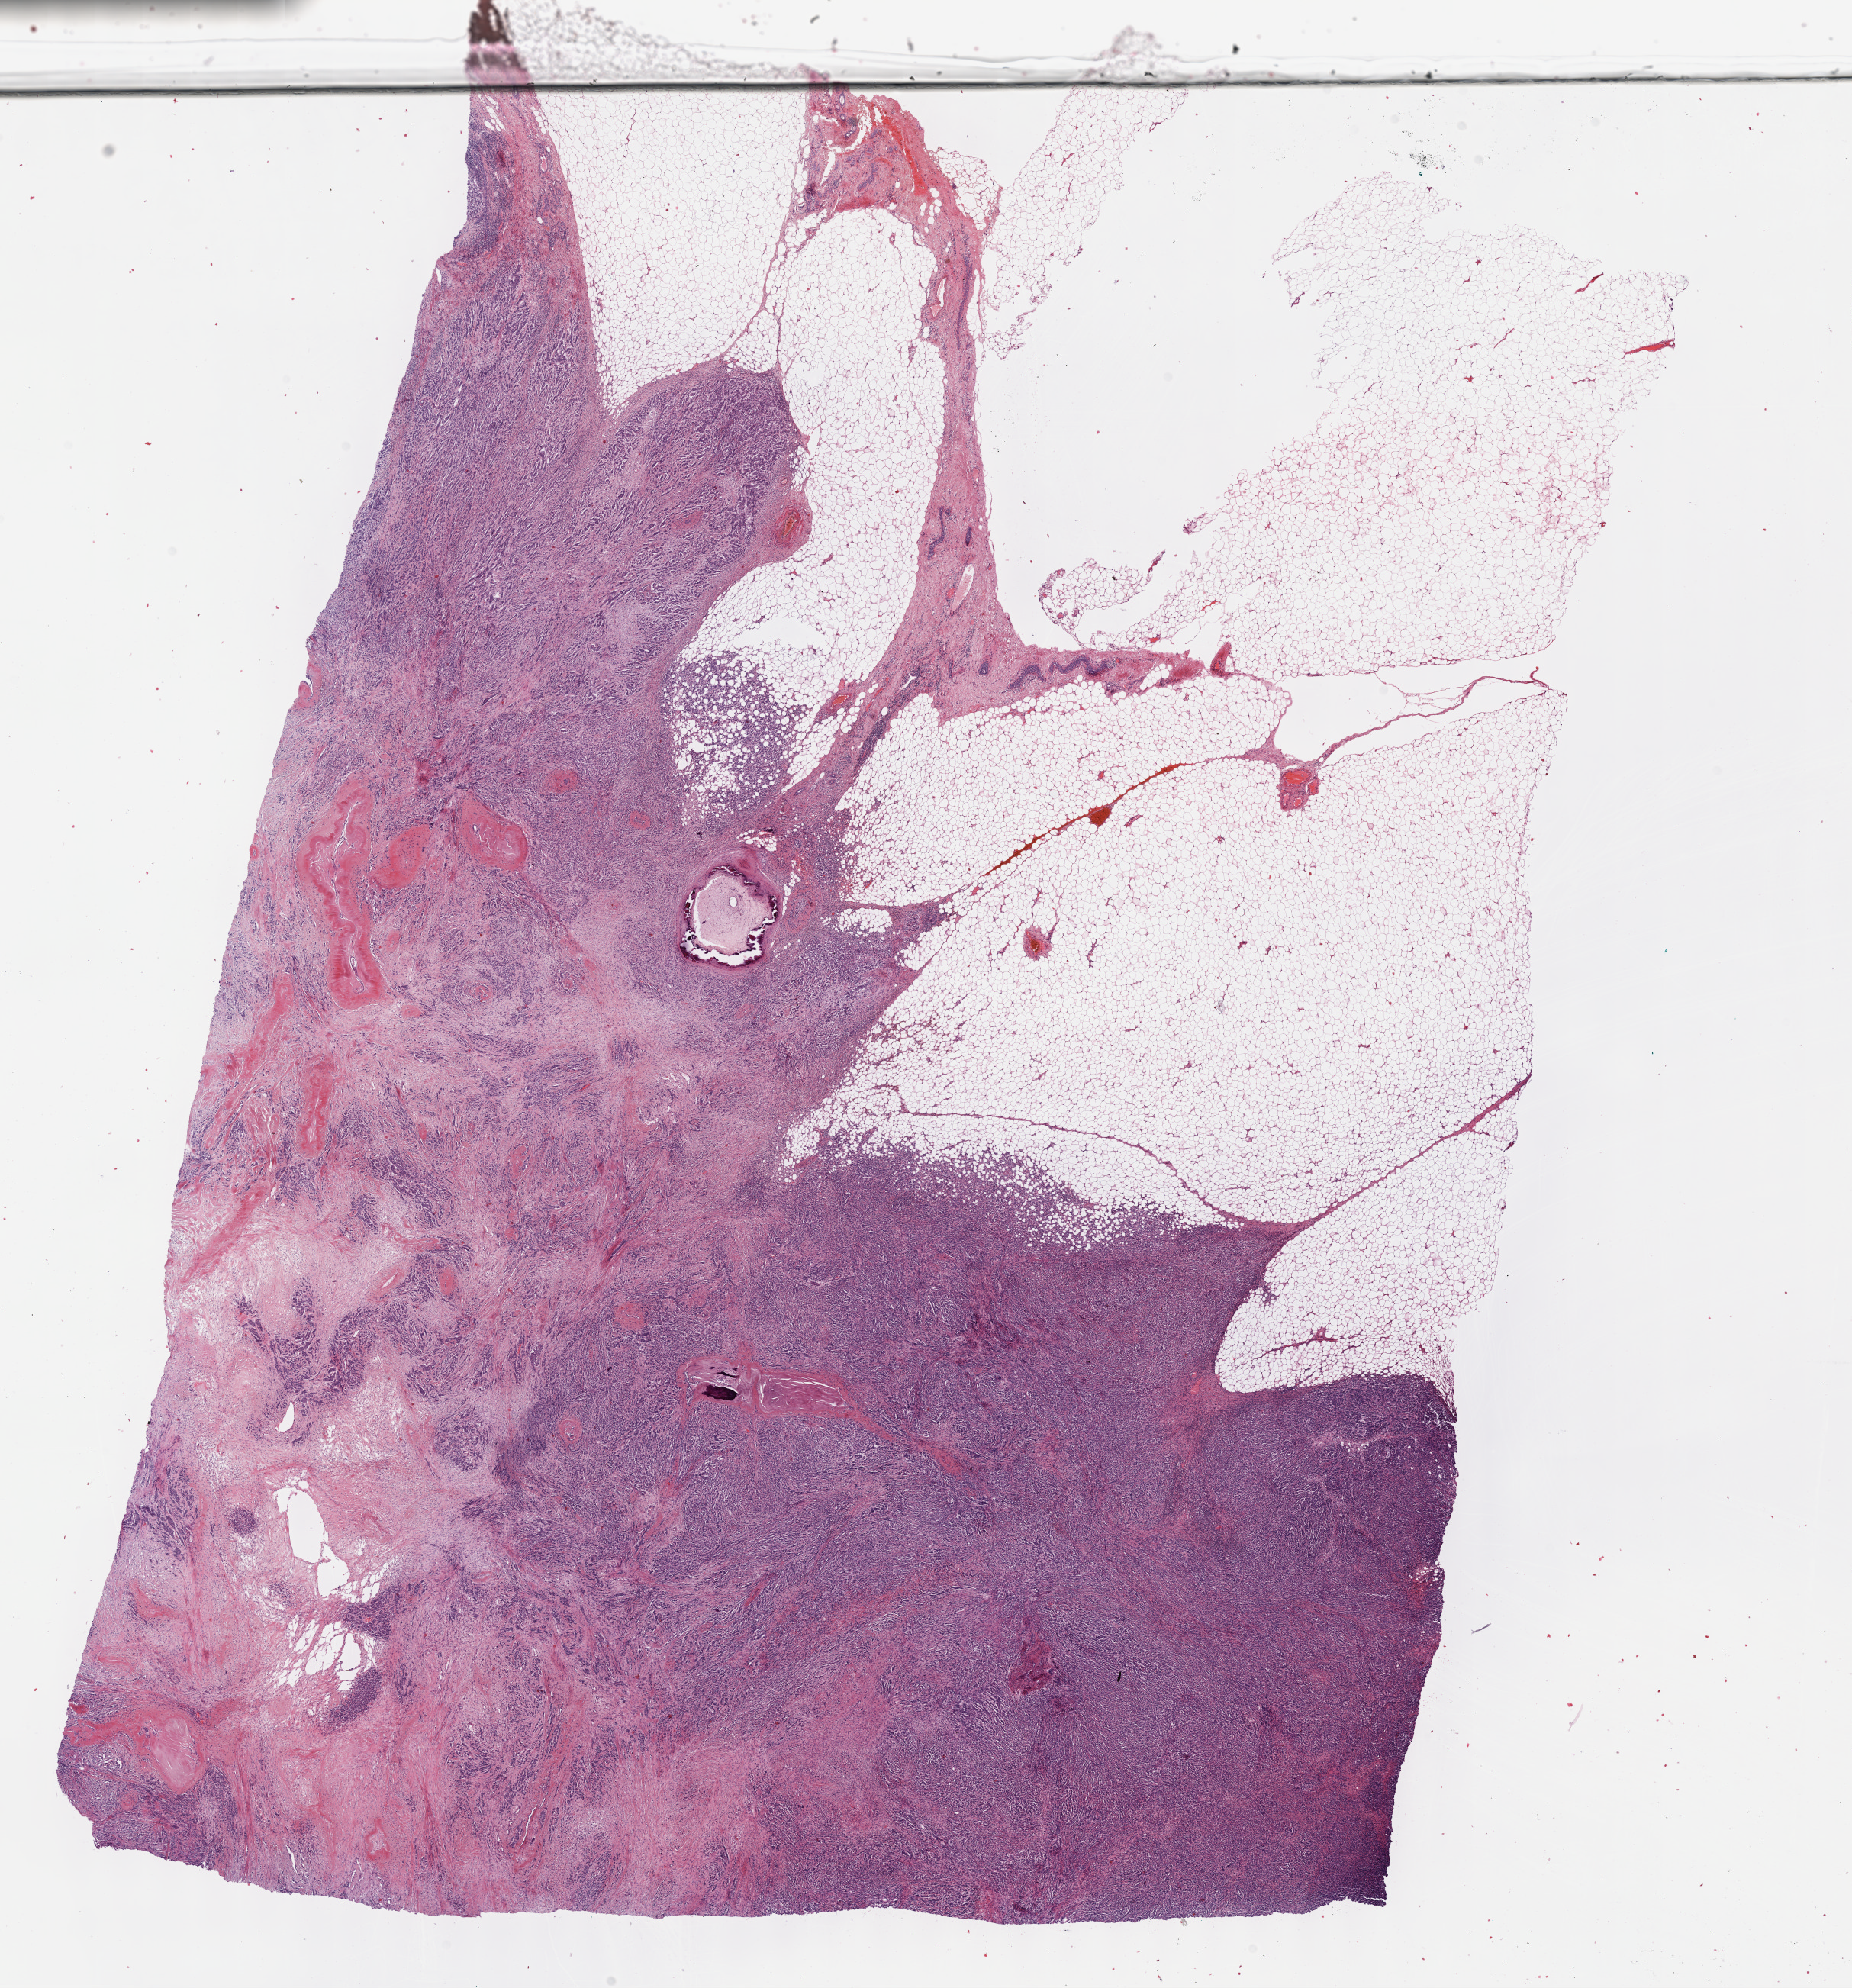
Digitized H&E tissue section (whole slide) — a low-resolution overview of the entire scanned area, about 19.6 x 21.1 mm, formalin-fixed paraffin-embedded (FFPE) diagnostic section, sample: primary tumour, breast. Female, age 80 years at initial diagnosis.
• laterality: left
• AJCC pathologic stage: IIIA (7th edition)
• histologic diagnosis: Infiltrating duct carcinoma, NOS